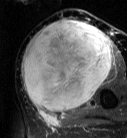
MRI of an extremity soft-tissue mass, one axial slice. Position 35 of 87 along the scan axis. T2-weighted fat-saturated. MR volume resampled by the dataset authors to the PET/CT grid (not the native acquisition matrix). 3.27 mm slice thickness. 127 × 138 image matrix, field of view 124 × 135 mm. Female patient. Case-level facts recorded for this patient, not image findings: histological type: pleiomorphic leiomyosarcoma; grade: high; site of the primary tumour: left biceps.
Outlined on this slice (expert contour drawn on MRI and transferred to this co-registered scan by the dataset authors):
- gross tumour volume including surrounding oedema: bounding box (x1, y1, x2, y2) in pixels: (22, 18, 112, 113)
- gross tumour volume (mass): (22, 20, 112, 113)